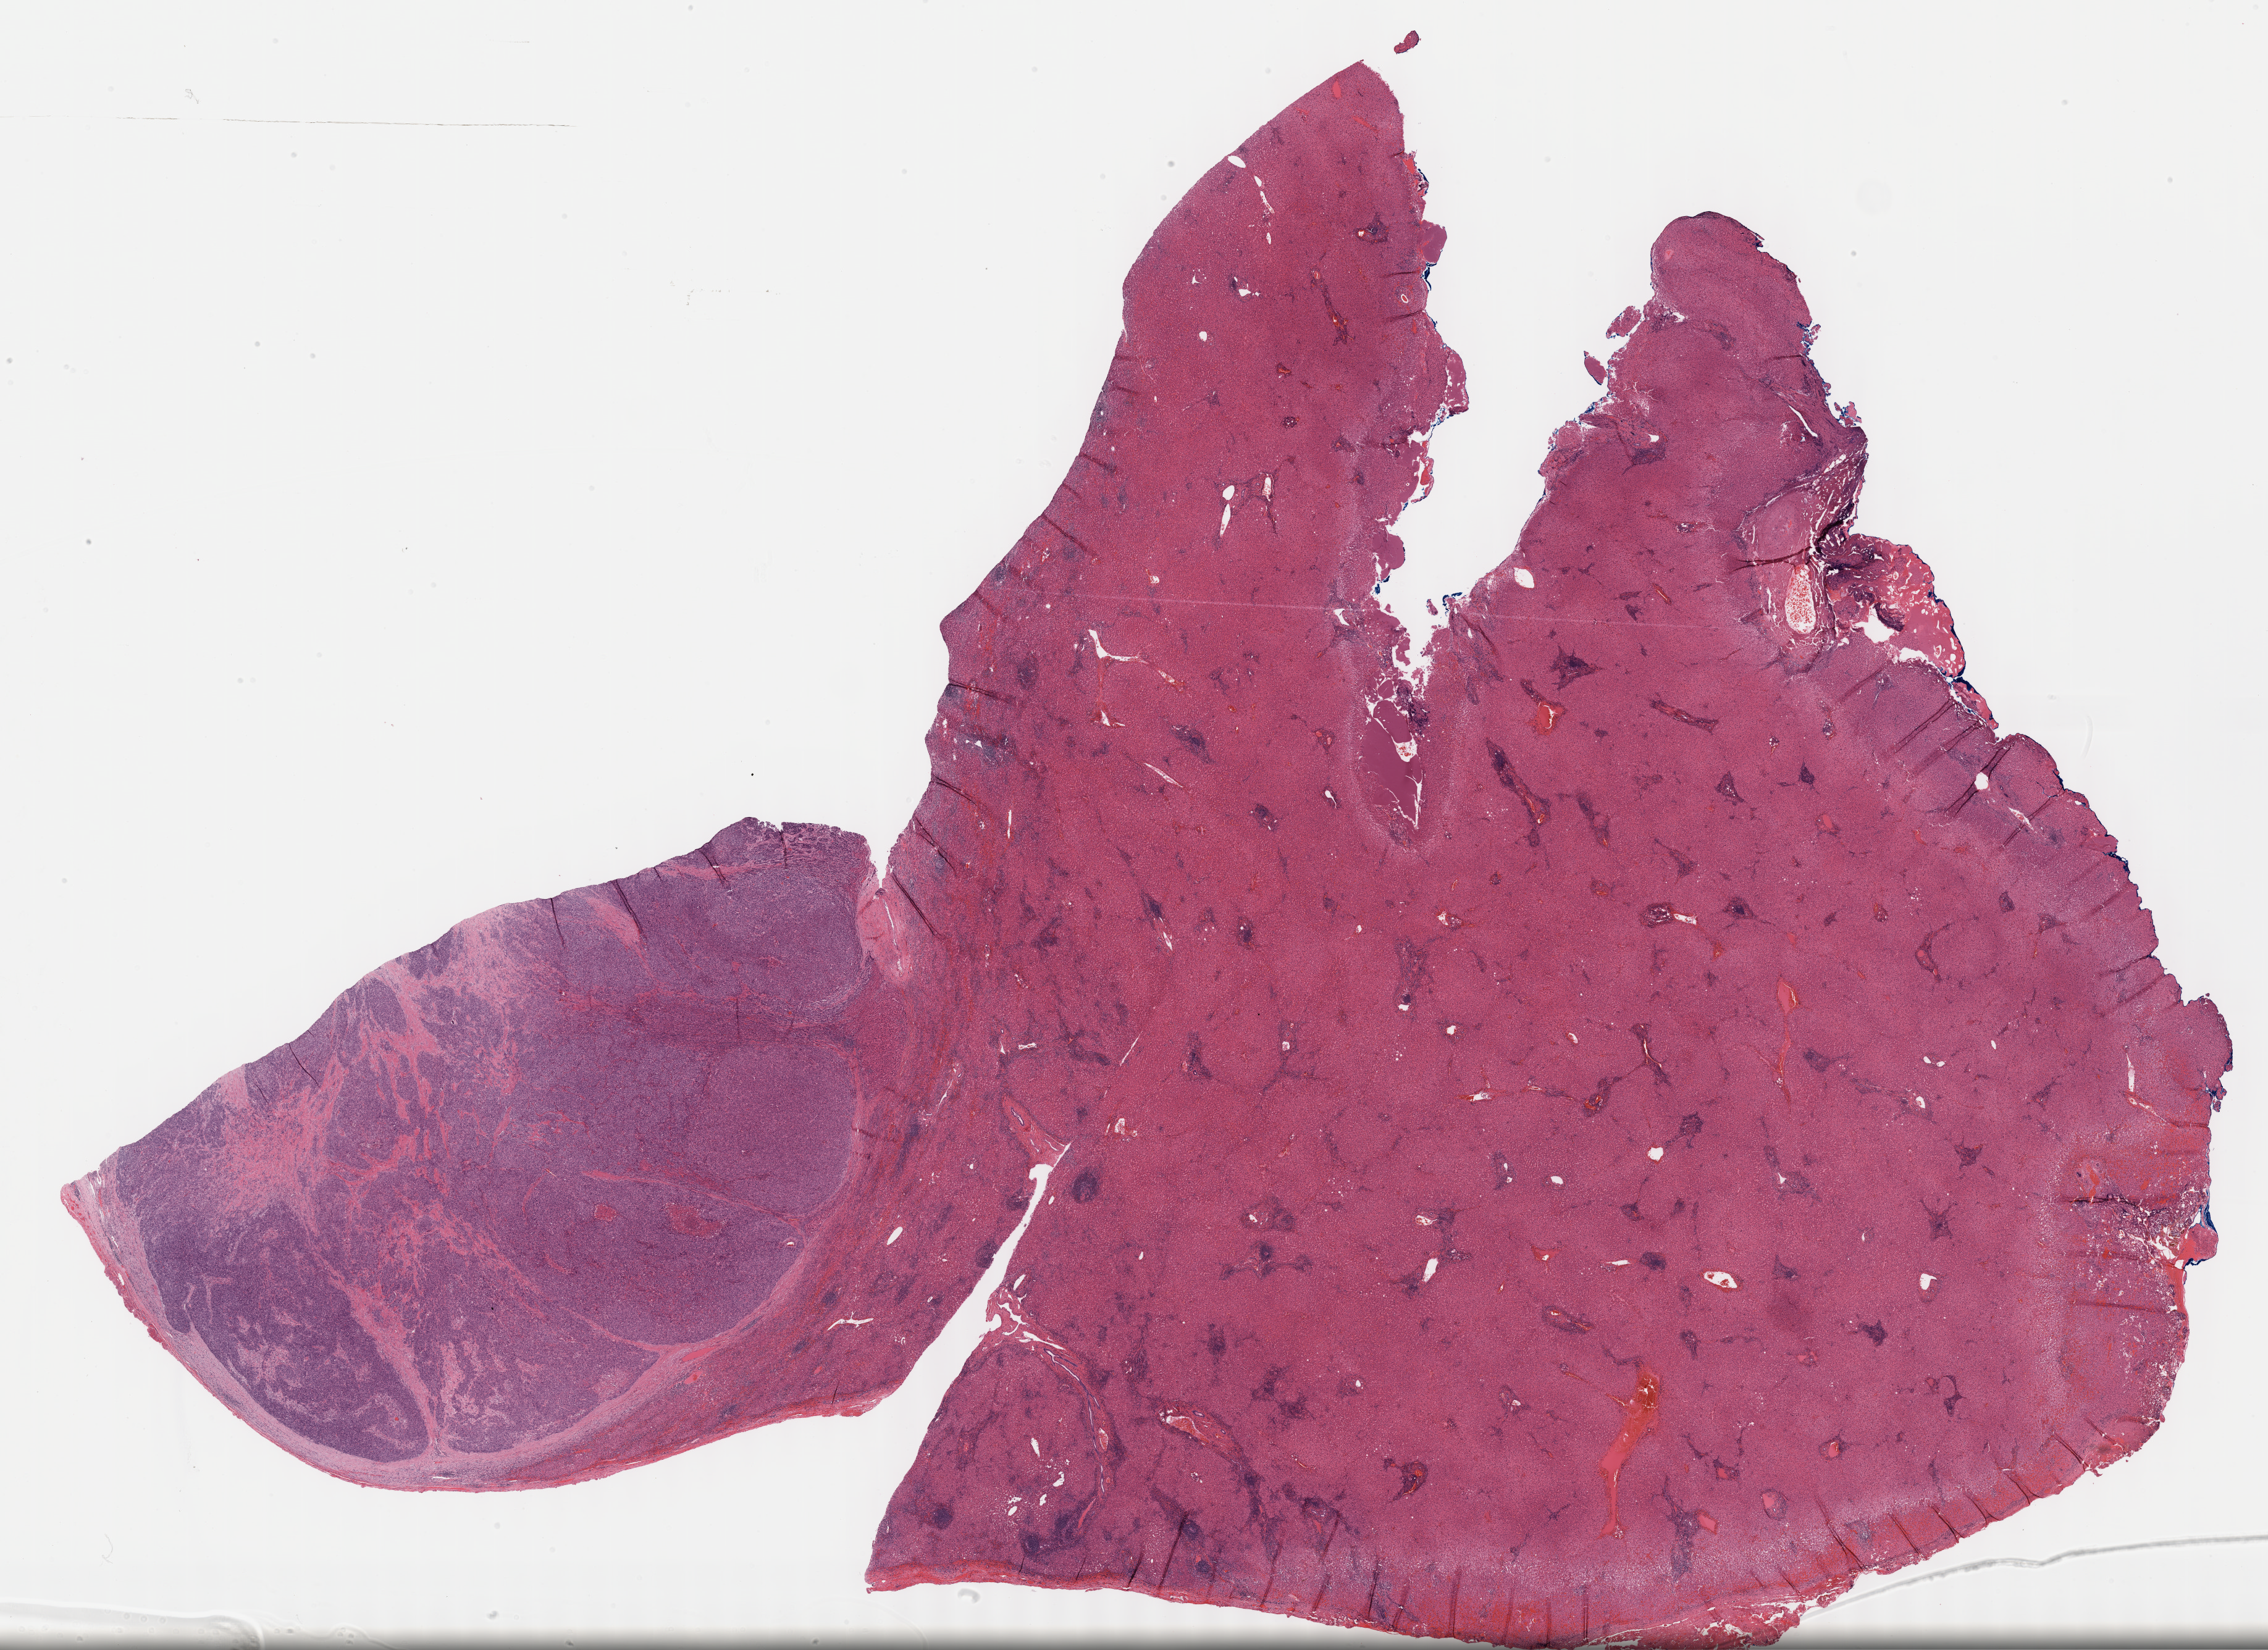
H&E whole-slide image, whole scanned area (about 29.7 x 21.6 mm) shown as a low-resolution overview. Formalin-fixed paraffin-embedded (FFPE) diagnostic section. Primary tumour sample from the liver. Patient: female, age at initial diagnosis 60 years. Histologic grade: G3 (poorly differentiated).
AJCC pathologic stage: I (7th edition). Pathologic diagnosis: Hepatocellular carcinoma, NOS.